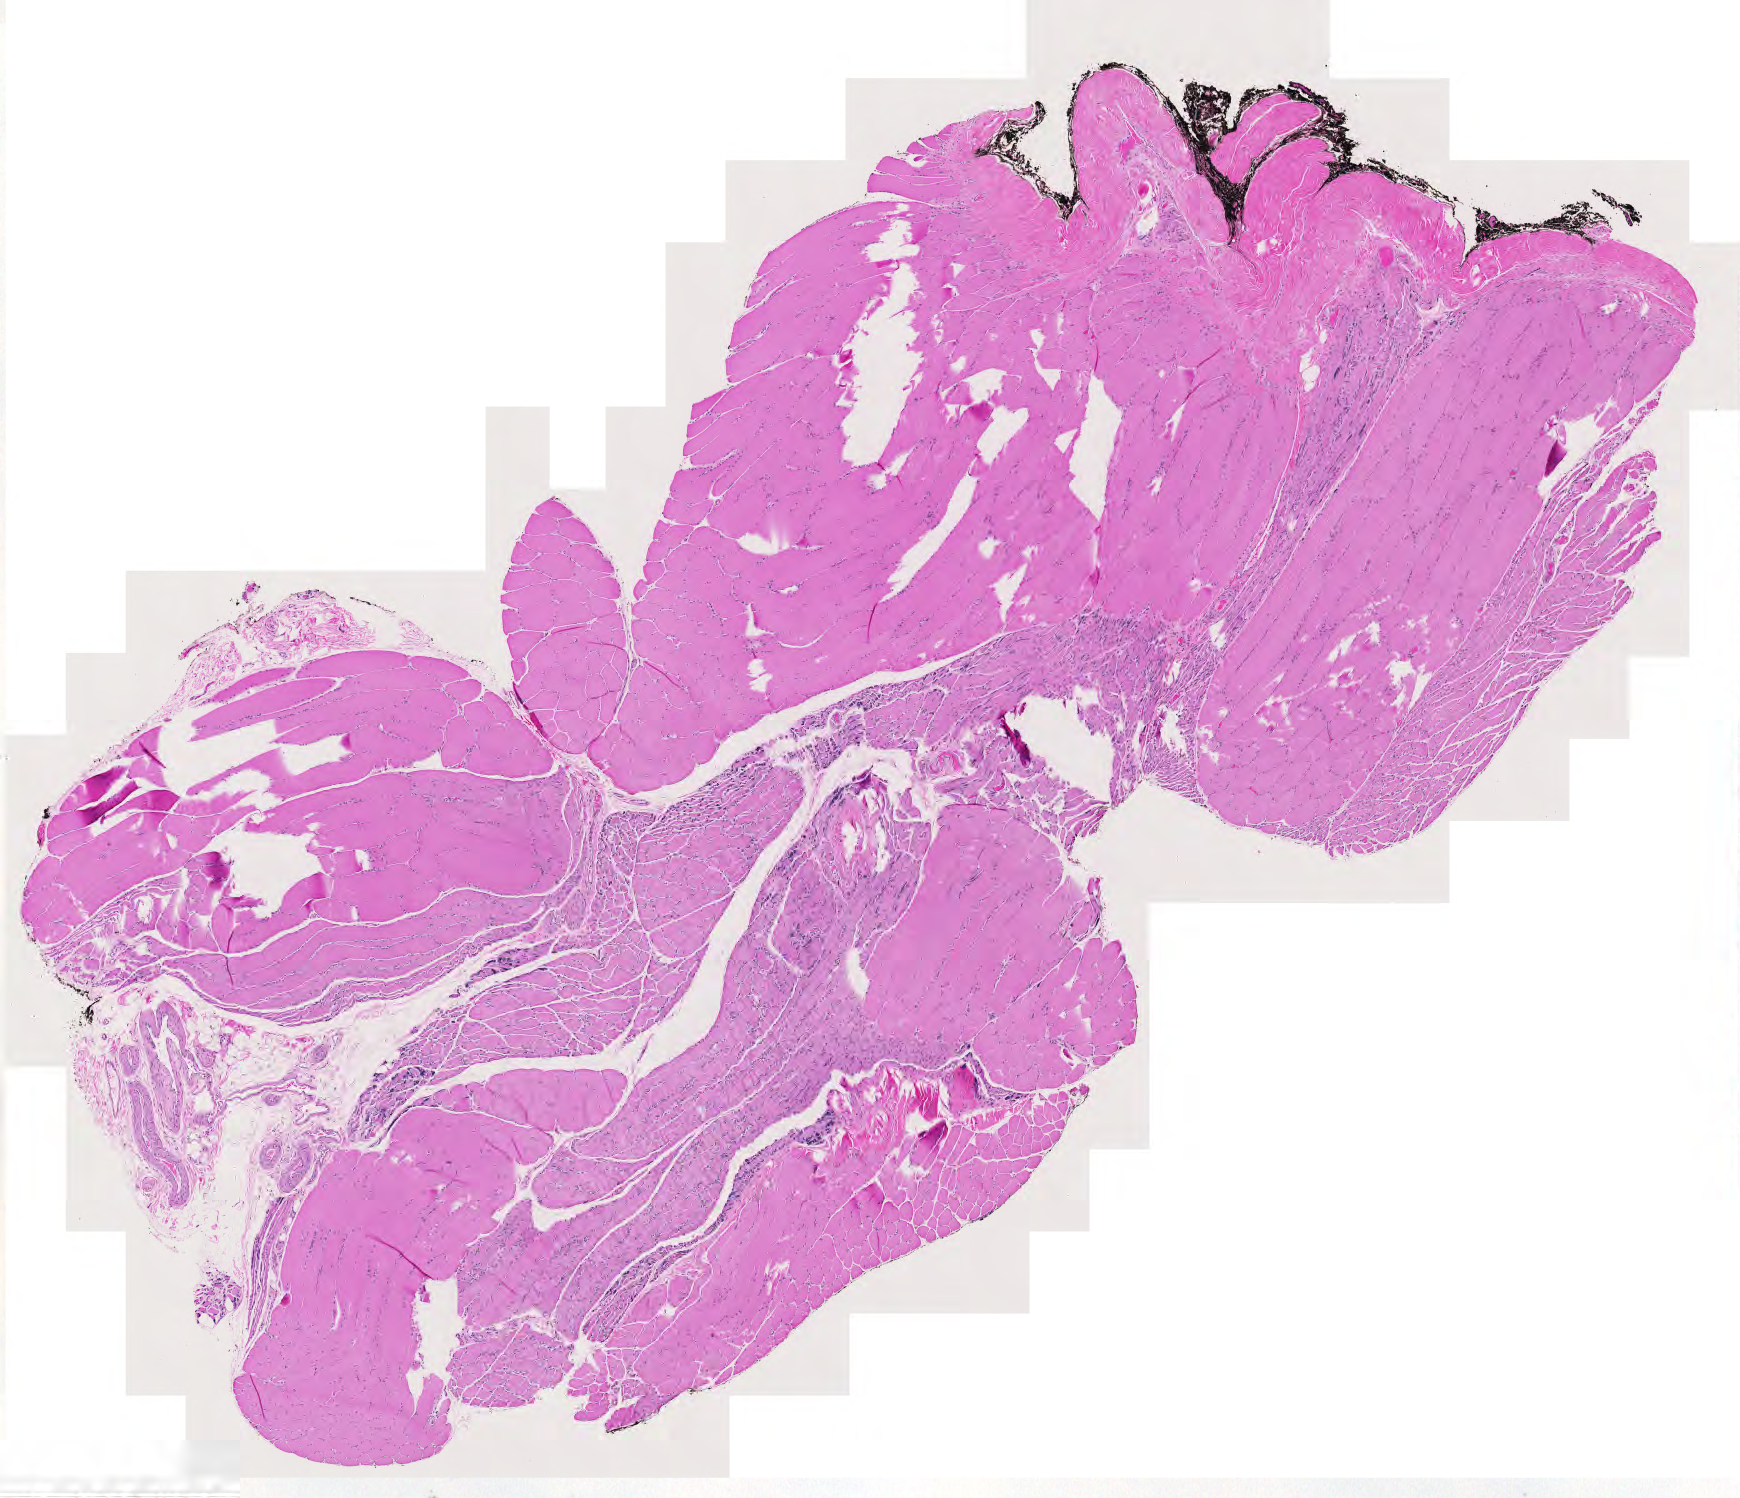
Whole-slide histology image, Hematoxylin and eosin (H&E) stained, low-resolution overview of the scanned area, about 9.0 x 7.7 mm, normal (non-tumour) tissue sample. Male, 49 y/o.
This section: normal (non-tumour) tissue from the same patient. Patient diagnosis (cohort enrolment): sarcoma (site not recorded at cohort level).